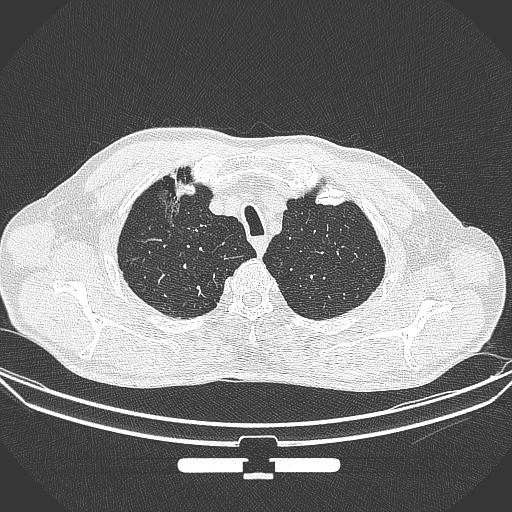
Chest CT, one axial slice. Slice 295 of 355 in the series (ordered by position). 120 kVp. Lung window (W 1500 / L -600 HU). 512 × 512 image matrix. Patient: male, 67 years. From the clinical record (not read from this slice): clinical TNM (as recorded): T1c N0 M0; histopathological grade: G2.
Annotated regions visible in this slice (rectangle marked by the reading radiologist):
- lung tumour (recorded histology: adenocarcinoma): bounding box (x1, y1, x2, y2) in pixels: (147, 180, 182, 234)